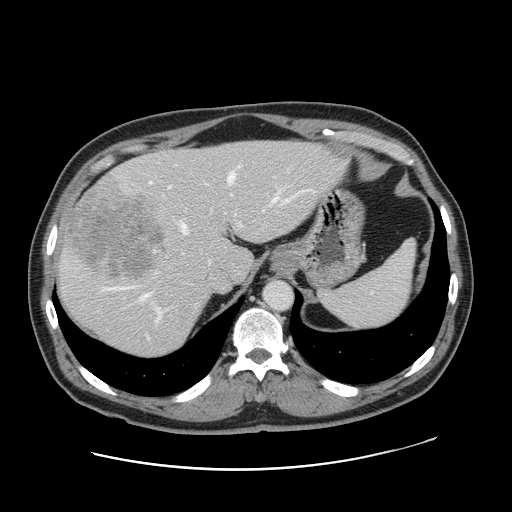
Contrast-enhanced abdominal CT, one axial slice. 120 kVp. Intravenous contrast given. Soft-tissue window (W 400 / L 40 HU). 512 × 512 image matrix, field of view 403 × 403 mm. Male patient, age 63 years. Case-level facts recorded for this patient, not image findings: diagnosis: colorectal cancer liver metastases, imaged before liver resection; multiple liver metastases: yes; largest metastasis: 8 cm; disease in both lobes: yes.
Annotated regions visible in this slice (outlined manually by an expert reader):
- hepatic veins: bounding box <106,172,278,300> (left, top, right, bottom; pixels)
- liver: <58,141,344,358>
- planned liver remnant (the part of the liver to remain after resection): <144,141,344,281>
- portal vein (with intrahepatic branches): <153,186,243,323>
- liver metastasis: <61,181,163,279>